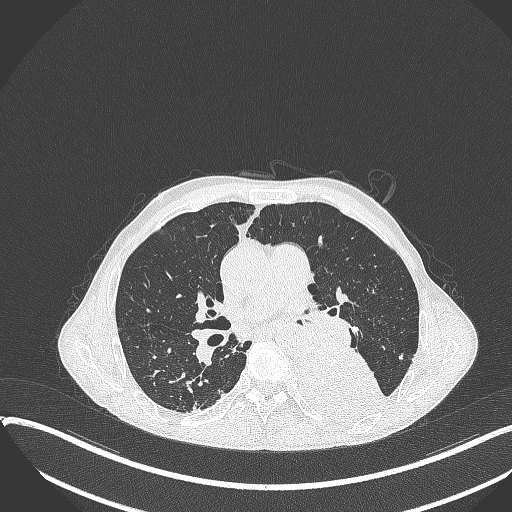
Chest CT, one axial slice. Position 209 of 401 along the scan axis. 120 kVp. Lung window (W 1500 / L -600 HU). 512 × 512 image matrix, field of view 400 × 400 mm. Patient: male, 57 years. From the clinical record (not read from this slice): clinical TNM (as recorded): T4 N0 M0.
Structures marked on this image (rectangle marked by the reading radiologist):
- lung tumour (recorded histology: squamous cell carcinoma): box from (x=291, y=341) to (x=389, y=428) px